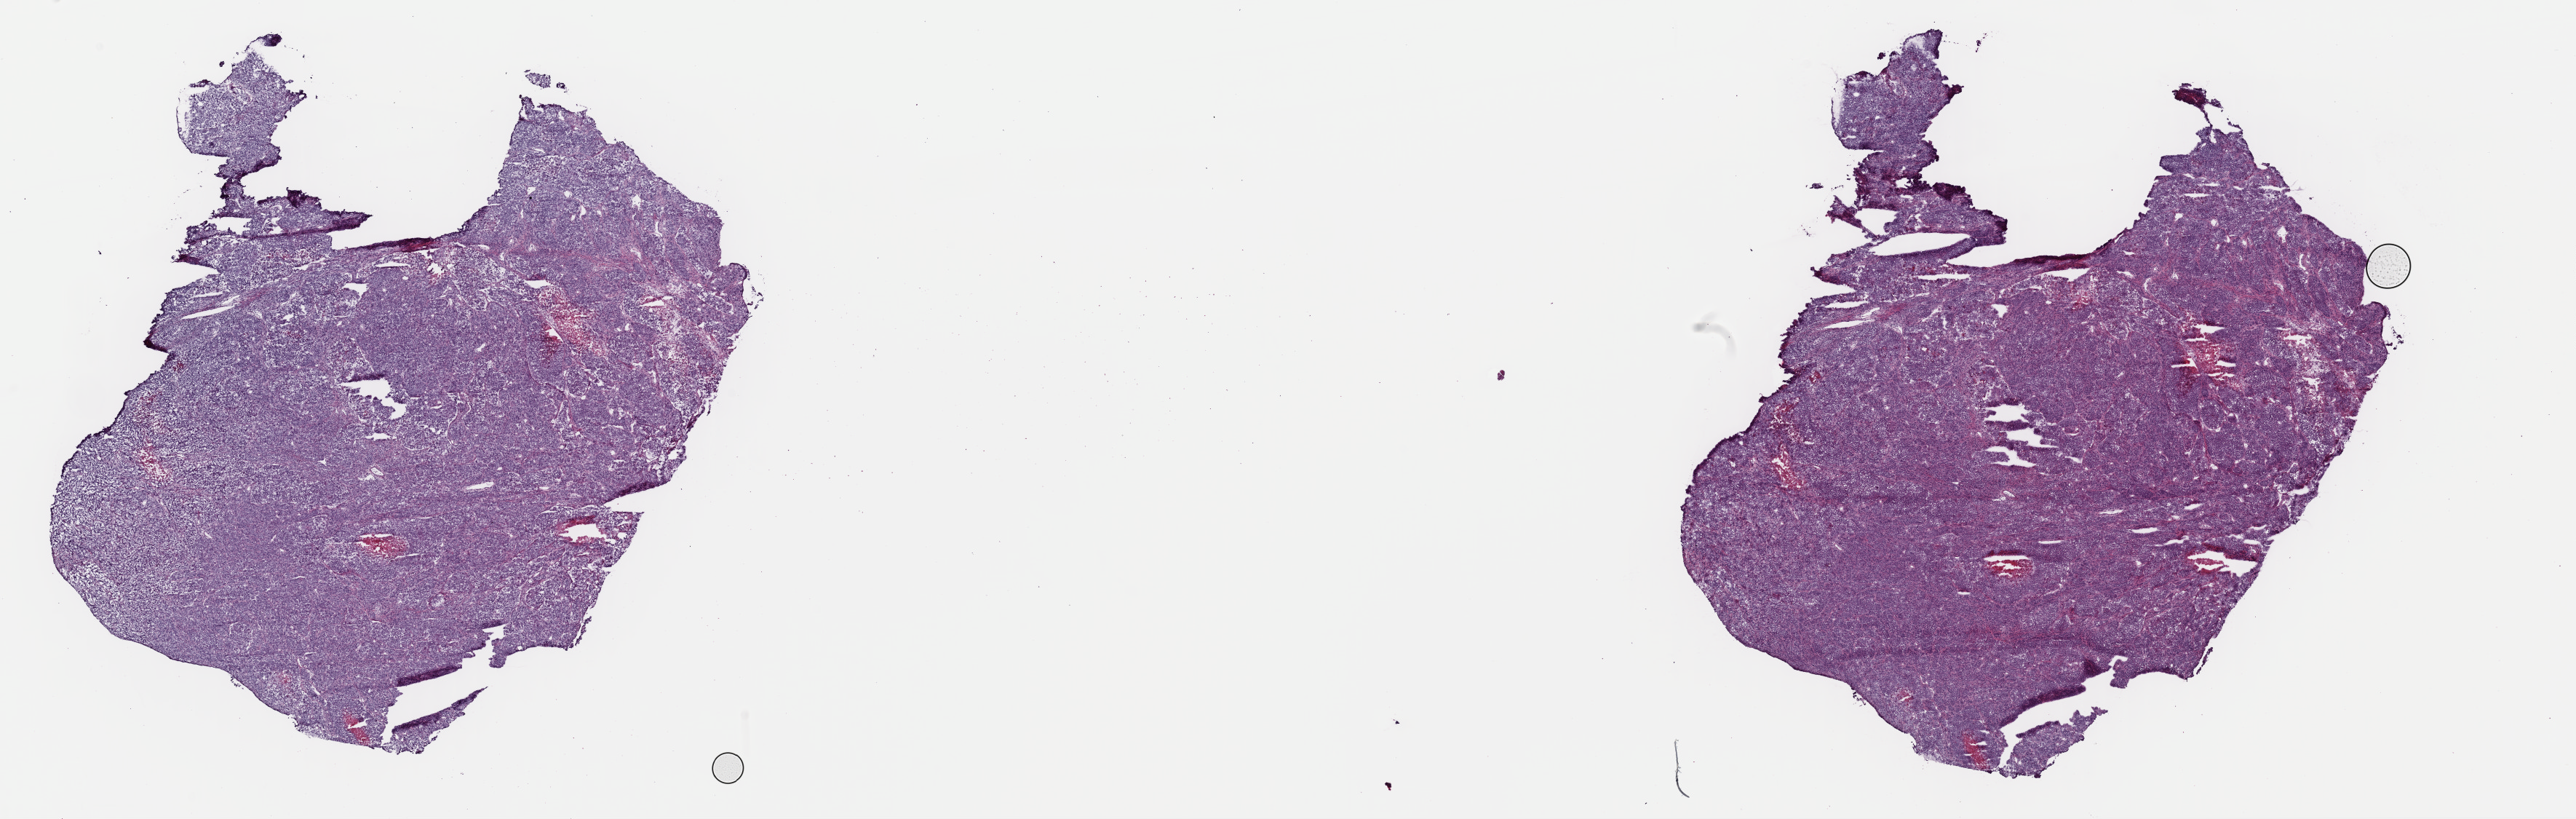
Whole-slide histology image, H&E, a low-resolution overview of the entire scanned area, about 28.0 x 8.9 mm (acquisition: 40x scan); frozen section; primary tumour sample from the uterus. Female patient; age at initial diagnosis 49 years. Histologic grade: G3 (poorly differentiated). Pathologist review of this section (percent, as recorded): tumour cells 100%, tumour nuclei 90%, normal cells 0%, stromal cells 0%, necrosis 0%. Inflammatory infiltration, as recorded: lymphocyte infiltration 0%, monocyte infiltration 0%, neutrophil infiltration 0%.
- FIGO stage: IVA
- histologic diagnosis: Endometrioid adenocarcinoma, NOS (endometrium)